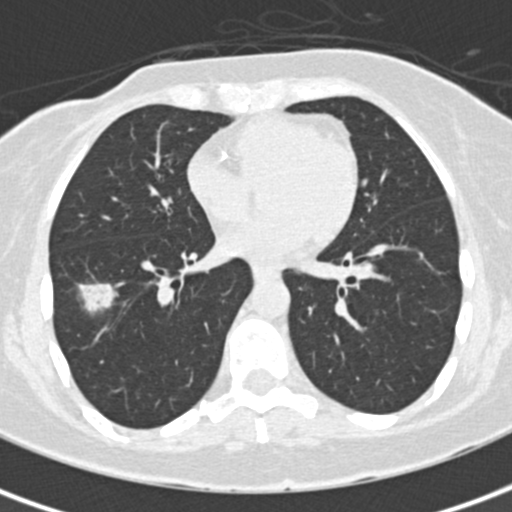
Axial slice from a low-dose chest CT screening exam; baseline annual screen; lung window (W 1500 / L -600 HU); 2 mm slice thickness; standard (soft-tissue) reconstruction kernel (B30f); slice 96 of 171 in the series. Female participant, aged 56 years at enrolment. Former smoker at enrolment.
Lesion marked by an expert reader, bounding box [x1, y1, x2, y2] px = [69, 273, 130, 328]. The screening reader recorded 5 non-calcified nodules or masses ≥4 mm on this exam; which of them this box marks is not recorded. Later outcome: lung cancer diagnosed 26 days after this screen — bronchiolo-alveolar carcinoma, mucinous, right lower lobe, well differentiated (G1), stage IA (AJCC 6th edition), 19 mm at pathology.